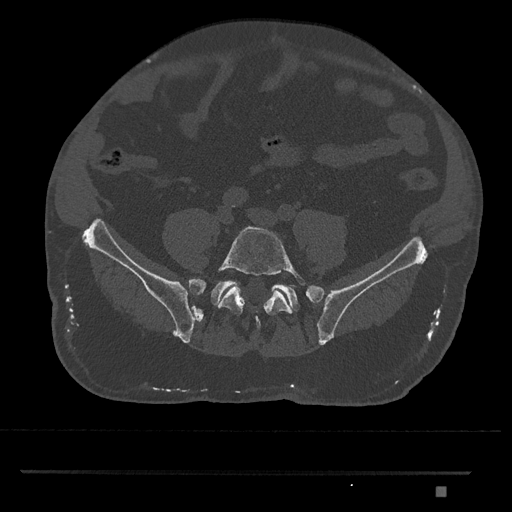
CT including the spine, one axial slice; position 544 of 1134 along the scan axis; reconstruction kernel Br40s/3; 120 kVp; bone window (W 1800 / L 400 HU); 0.5 mm slice thickness; 512 × 512 image matrix. Patient: male, 65 years. From the clinical record (not read from this slice): primary cancer: prostate.
Outlined on this slice (semi-automatic segmentation, software-assisted and operator-edited):
- L5 vertebra: bounding box <213,226,309,330> (left, top, right, bottom; pixels)